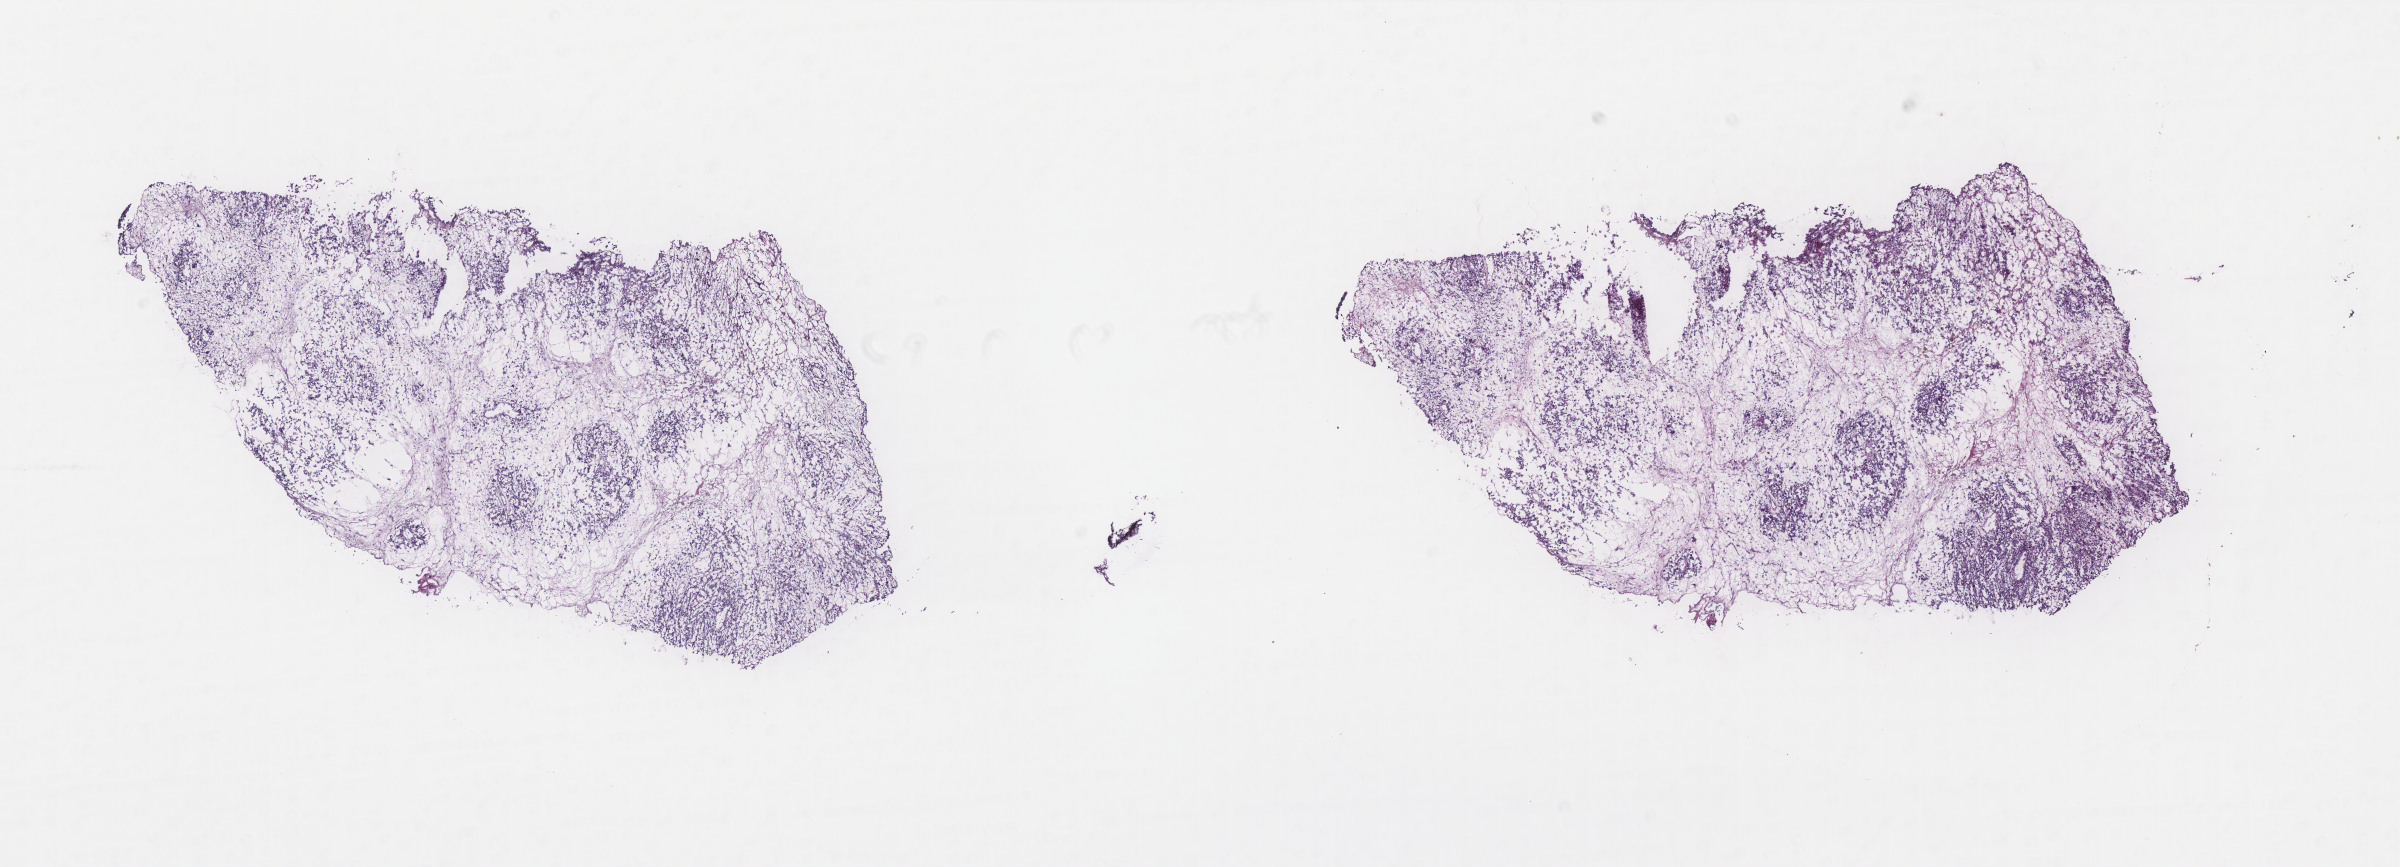
Digitized H&E tissue section (whole slide), shown as a low-resolution overview of the whole scanned area (about 19.2 x 7.0 mm). Frozen section from the top of the tissue portion. Metastatic tumour sample, sampled site not recorded. Male patient; age at initial diagnosis 51 years. Pathologist review of this section (percent, as recorded): tumour cells 100%, tumour nuclei 70%, normal cells 0%, stromal cells 0%, necrosis 0%. Infiltration values recorded for this section: lymphocyte infiltration 0%, monocyte infiltration 0%, neutrophil infiltration 0%.
This section: metastatic tumour tissue. Patient diagnosis: Acral lentiginous melanoma, malignant.